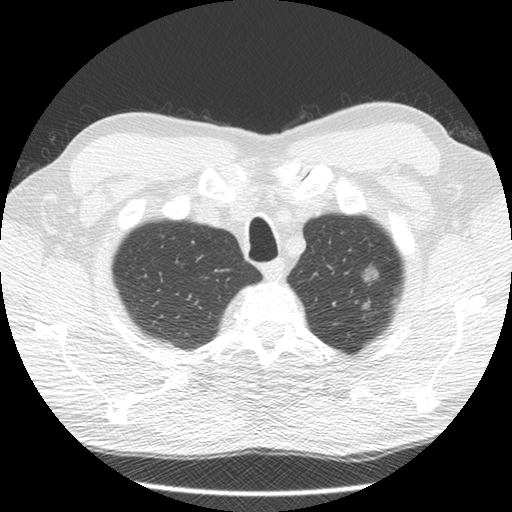
Low-dose screening chest CT, one axial slice; position 119 of 132 along the scan axis; reconstruction kernel STANDARD; 120 kVp; lung window (W 1500 / L -600 HU); 2.5 mm slice thickness; 512 × 512 image matrix.
Annotated regions visible in this slice (expert manual segmentation):
- lesion 1 (tumor, upper lobe of left lung): bounding box <363,267,379,286> (left, top, right, bottom; pixels)